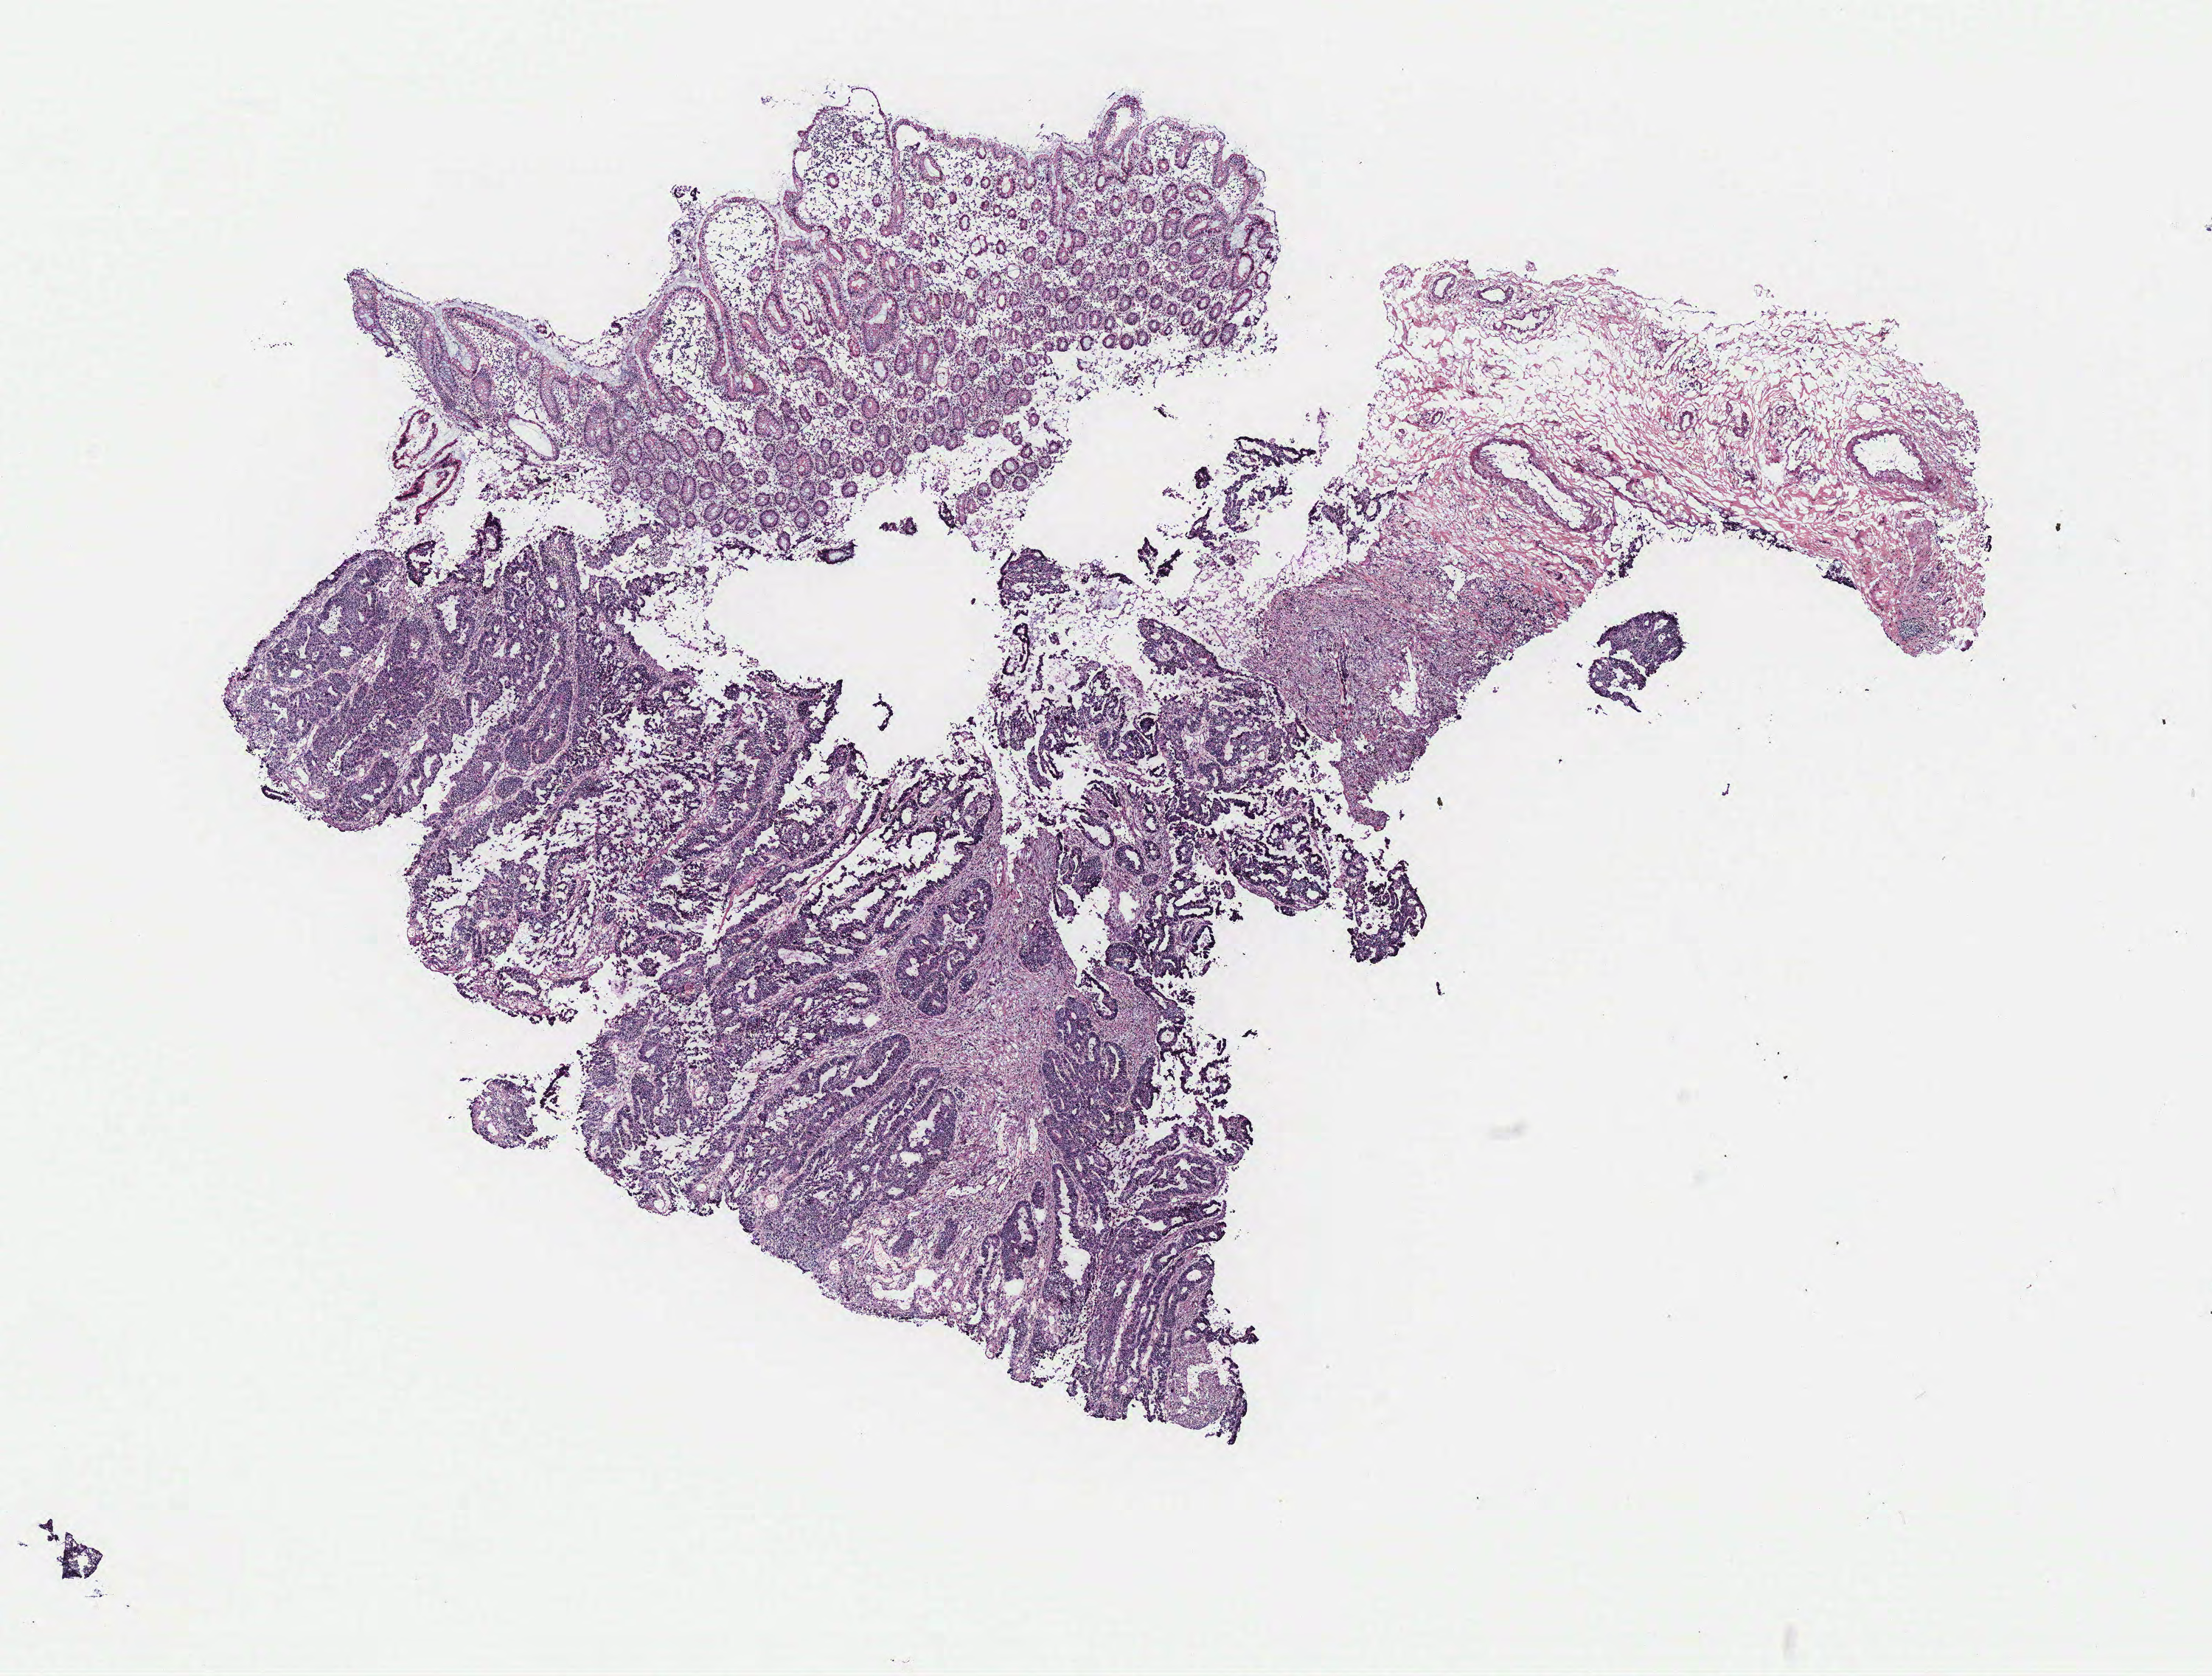
H&E-stained whole-slide image — low-resolution overview of the scanned area, about 12.0 x 9.1 mm (from a 40x scan); tumour tissue sample, colon. Patient: female, aged 90 or older.
- primary tumour site (as recorded): colon
- AJCC pathologic stage: IIA
- diagnosis: Adenocarcinoma, NOS